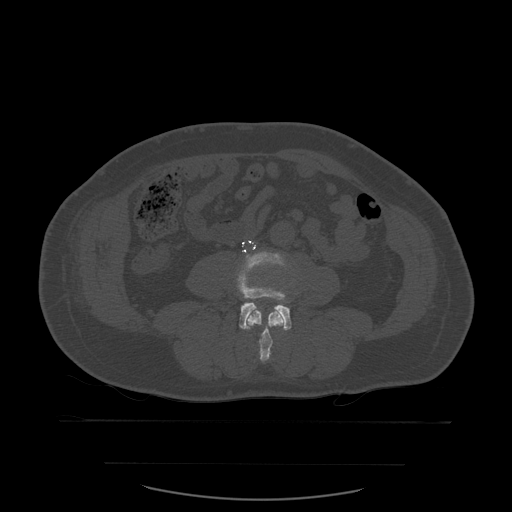
CT including the spine, one axial slice. Slice 177 of 590 in the series (ordered by position). Bone window (W 1800 / L 400 HU). 1.25 mm slice thickness. 512 × 512 image matrix. Patient age 71 years. From the clinical record (not read from this slice): primary cancer: lung.
Annotated regions visible in this slice (semi-automatic segmentation, software-assisted and operator-edited):
- L3 vertebra: bounding box (x1, y1, x2, y2) in pixels: (247, 284, 285, 363)
- L4 vertebra: (238, 252, 292, 331)